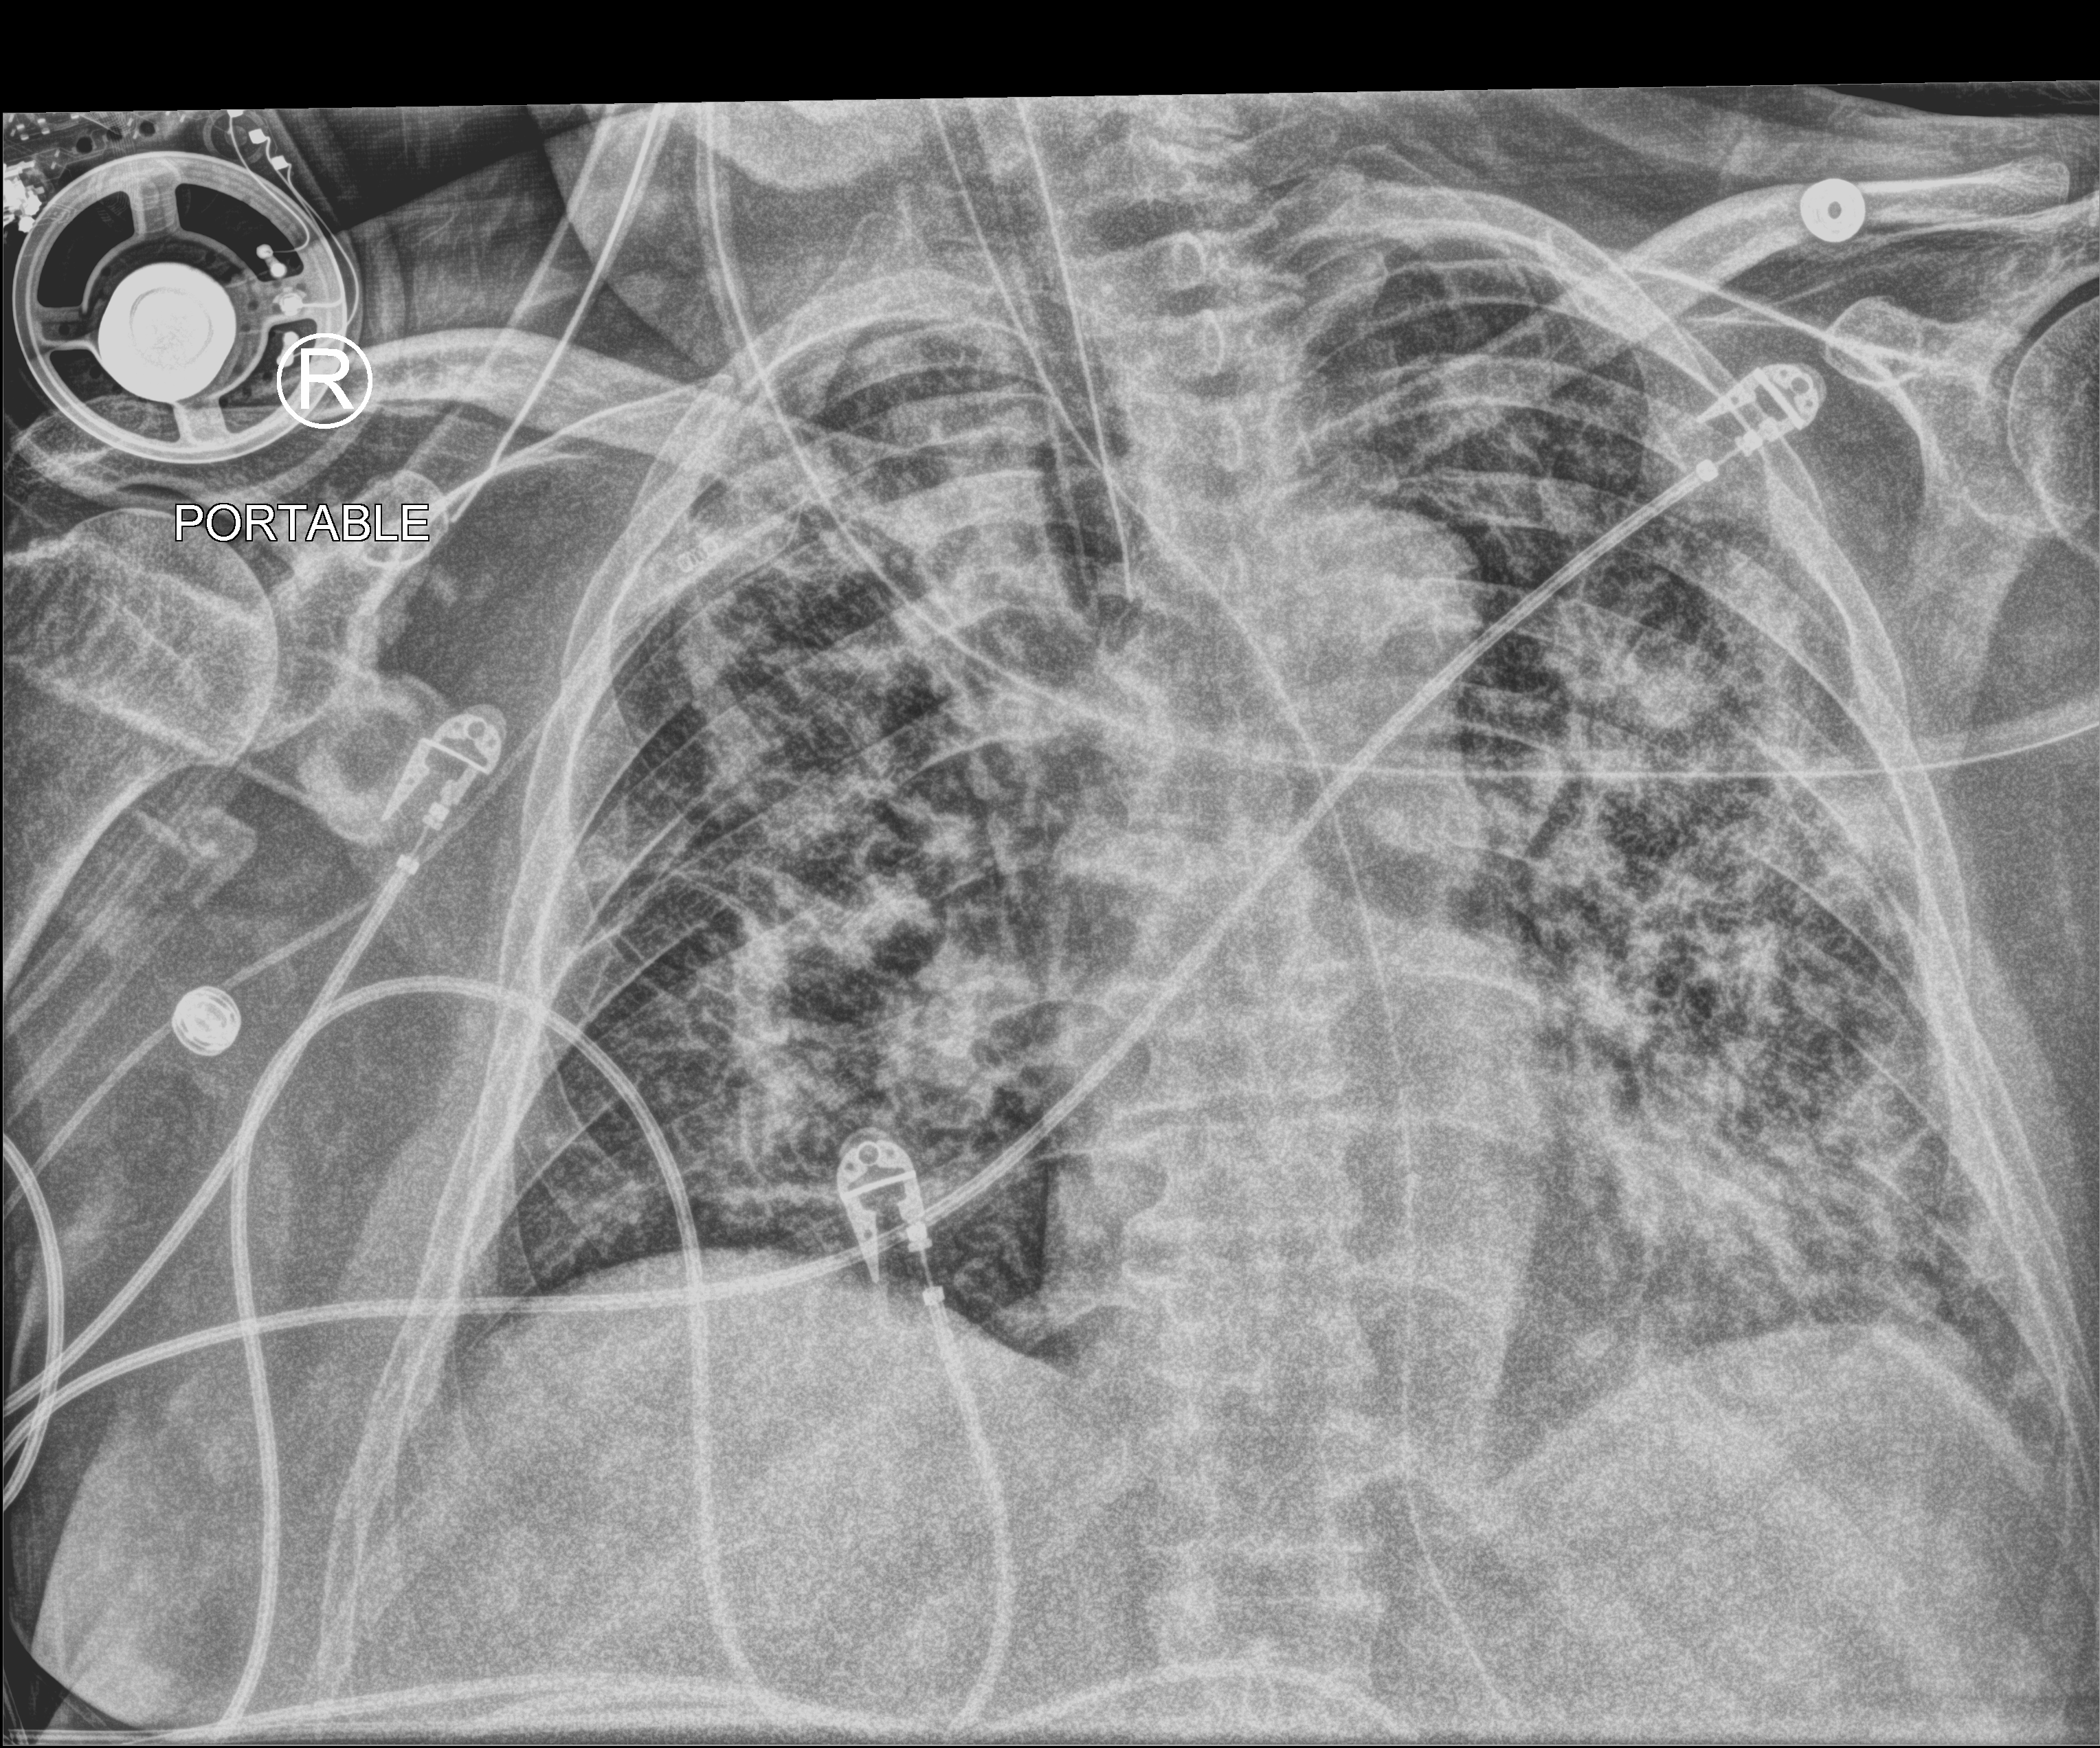
Bedside chest radiograph (computed radiography); anteroposterior (AP) projection. Patient hospitalised with COVID-19; male, aged 60–74 years.
Hospital-stay facts (about this admission, not read from this image; timing relative to this image not recorded):
- hypertension (admission record): no